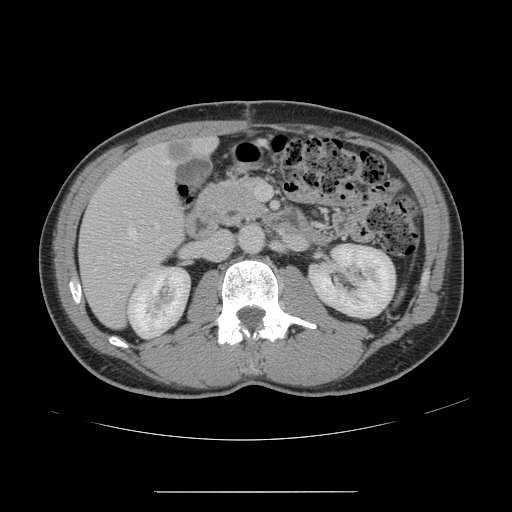
Contrast-enhanced abdominal CT, one axial slice; intravenous contrast given; soft-tissue window (W 400 / L 40 HU); 2.5 mm slice thickness; 512 × 512 image matrix. Male patient, age 53 years. Case-level facts recorded for this patient, not image findings: diagnosis: colorectal cancer liver metastases, imaged before liver resection; multiple liver metastases: yes; largest metastasis: 2.4 cm; chemotherapy before resection: yes.
Annotated regions visible in this slice (manually delineated by an expert):
- hepatic veins: bounding box <94,160,170,271> (left, top, right, bottom; pixels)
- liver: <81,139,213,326>
- planned liver remnant (the part of the liver to remain after resection): <199,139,214,153>
- portal vein (with intrahepatic branches): <137,185,267,199>
- liver metastasis: <167,142,193,161>